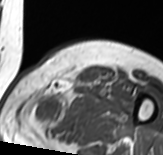
MRI of an extremity soft-tissue mass, one axial slice; position 49 of 65 along the scan axis; MR volume resampled by the dataset authors to the PET/CT grid (not the native acquisition matrix); 163 × 155 image matrix. Female patient. Case-level facts recorded for this patient, not image findings: histological type: pleomorphic leiomyosarcoma; grade: high; site of the primary tumour: left thigh.
Structures marked on this image (expert contour drawn on MRI and transferred to this co-registered scan by the dataset authors):
- gross tumour volume including surrounding oedema: box from (x=26, y=79) to (x=90, y=135) px